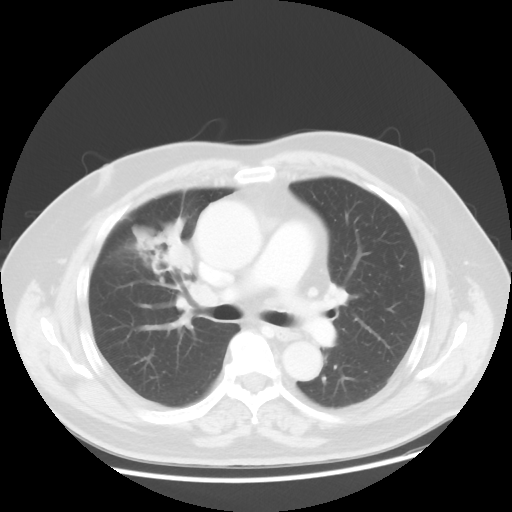
Chest CT, one axial slice; slice 28 of 48 in the series (ordered by position); lung window (W 1500 / L -600 HU); 5 mm slice thickness; 512 × 512 image matrix. Patient: male, 60 years. Case-level facts recorded for this patient, not image findings: clinical TNM (as recorded): T2 N3 M0.
Structures marked on this image (bounding box drawn by a radiologist):
- lung tumour (recorded histology: adenocarcinoma): bounding box (x1, y1, x2, y2) in pixels: (132, 213, 190, 279)